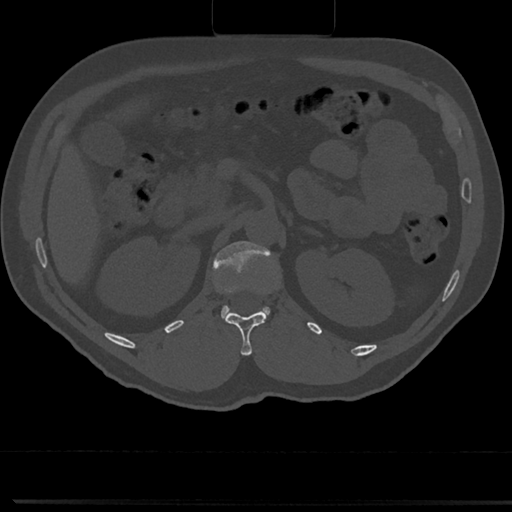
CT including the spine, one axial slice; slice 116 of 817 in the series (ordered by position); bone window (W 1800 / L 400 HU); 0.5 mm slice thickness; 512 × 512 image matrix, field of view 355 × 355 mm. Male patient, age 61 years. From the clinical record (not read from this slice): primary cancer: prostate.
Annotated regions visible in this slice (semi-automatic segmentation, software-assisted and operator-edited):
- L1 vertebra: box from (x=212, y=240) to (x=277, y=324) px
- T12 vertebra: (x=223, y=310)–(x=268, y=355)